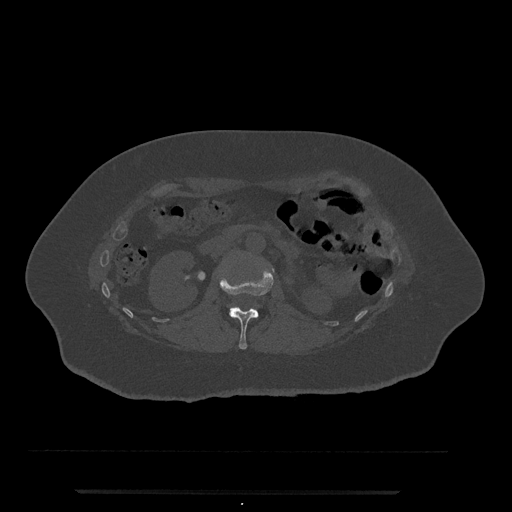
CT including the spine, one axial slice. Reconstruction kernel Br40s/3. 120 kVp. Bone window (W 1800 / L 400 HU). 512 × 512 image matrix, field of view 440 × 440 mm. Female patient, age 51 years. Case-level facts recorded for this patient, not image findings: primary cancer: neuro.
Annotated regions visible in this slice (semi-automatically segmented with operator editing):
- L1 vertebra: bounding box <219,268,274,350> (left, top, right, bottom; pixels)
- L2 vertebra: <229,306,237,309>